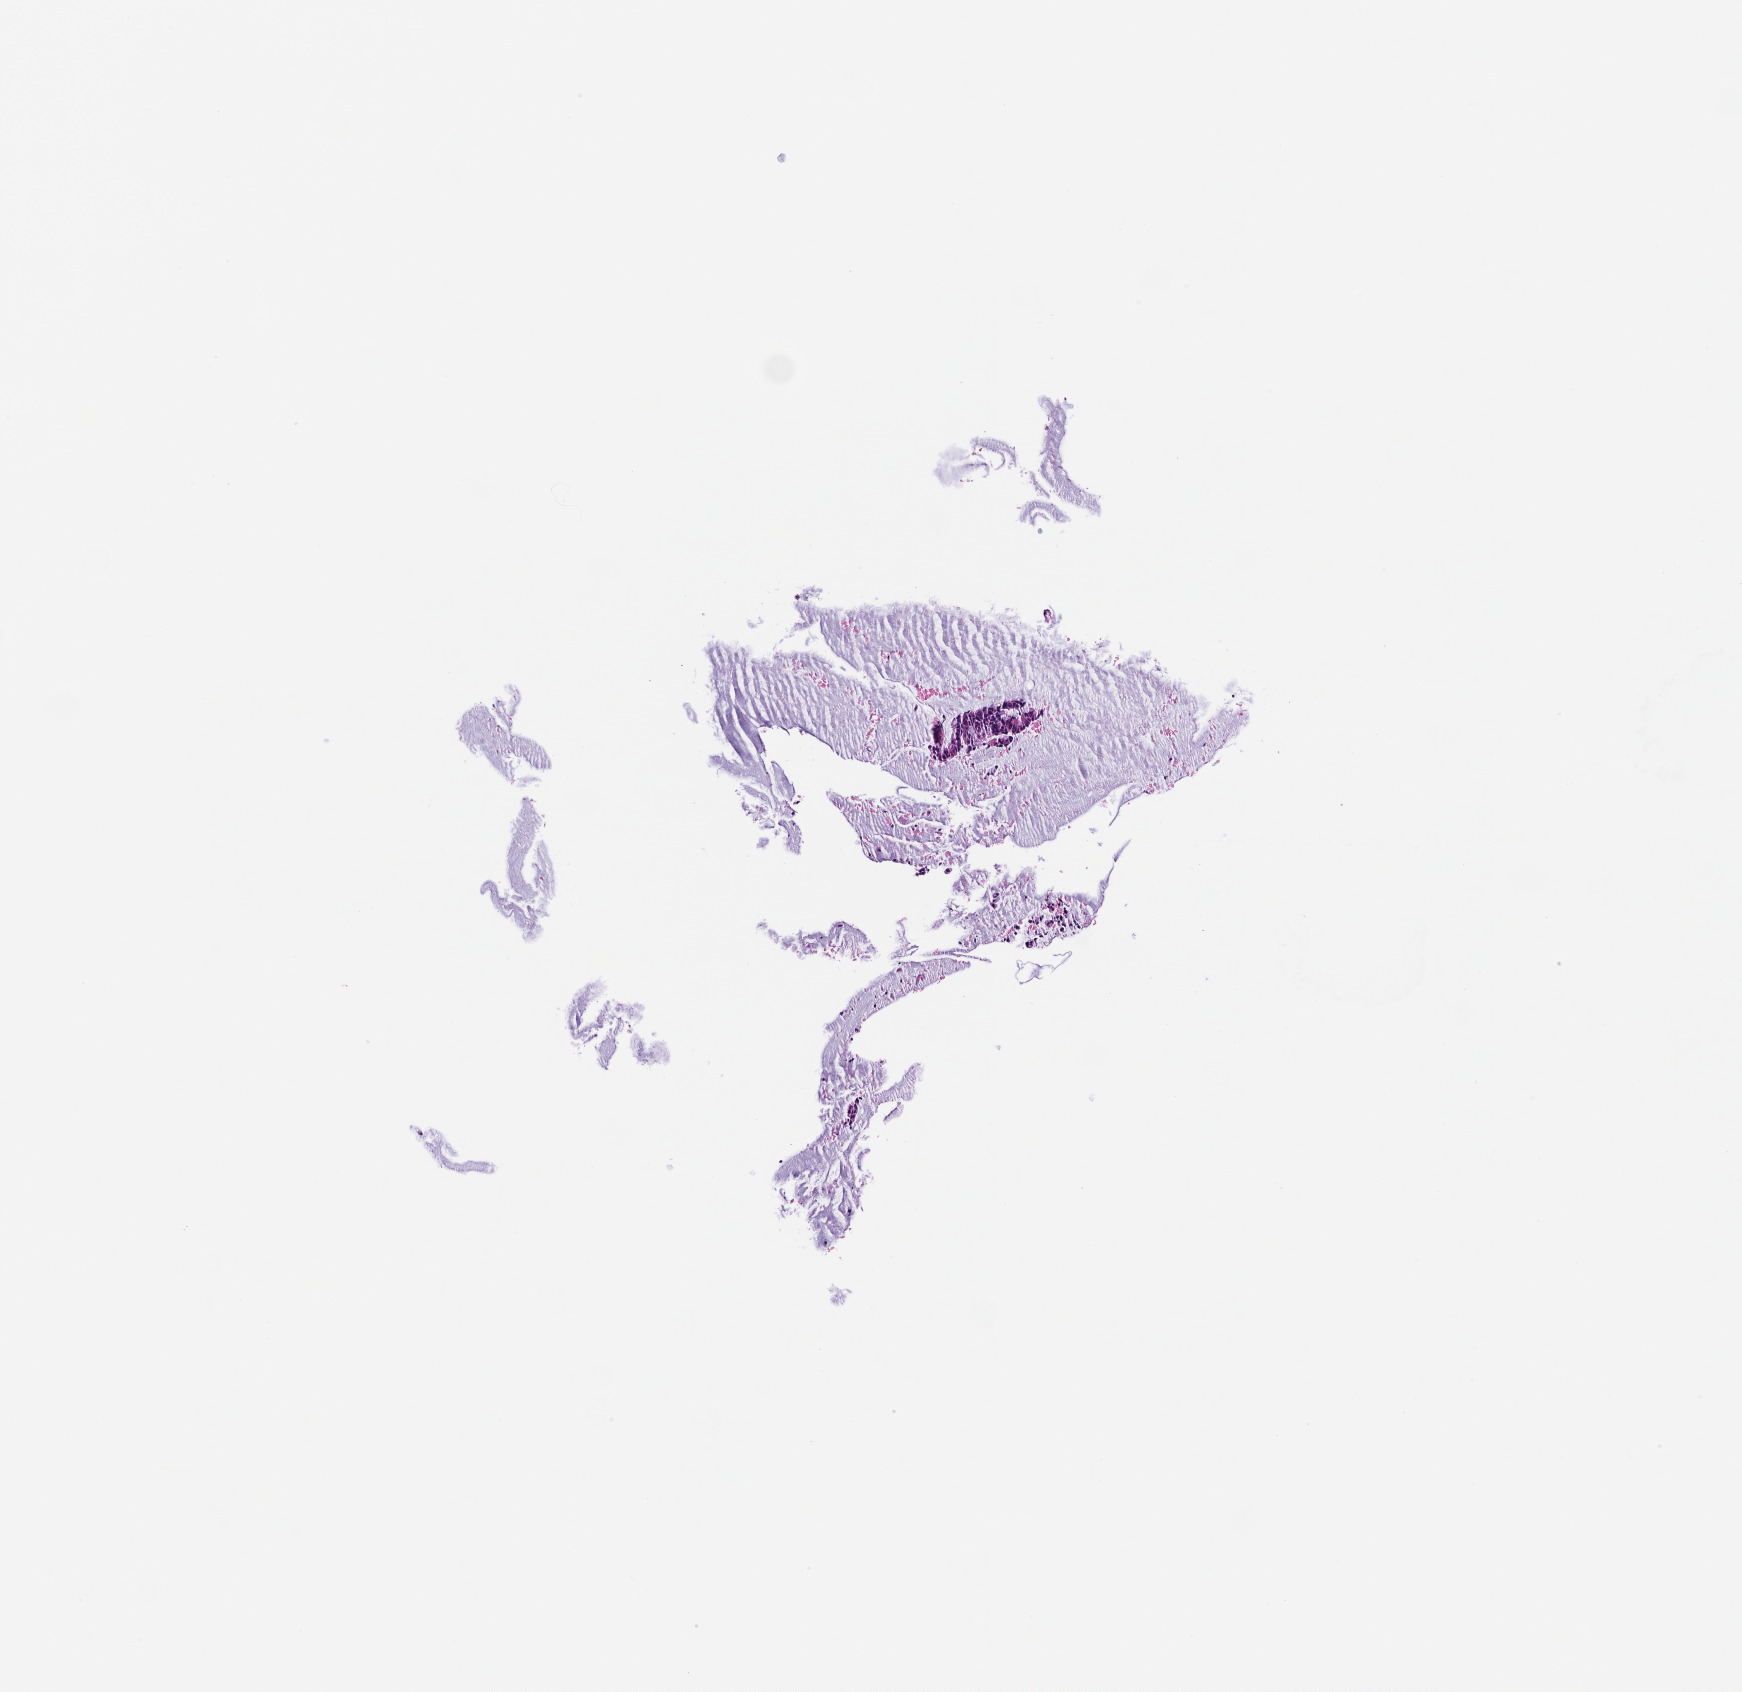
H&E whole-slide image — low-resolution overview of the scanned area, about 3.5 x 3.4 mm; formalin-fixed paraffin-embedded section. Patient: male.
This section: metastasis (sampled organ not recorded). Primary diagnosis of the patient: Colorectal Carcinoma.